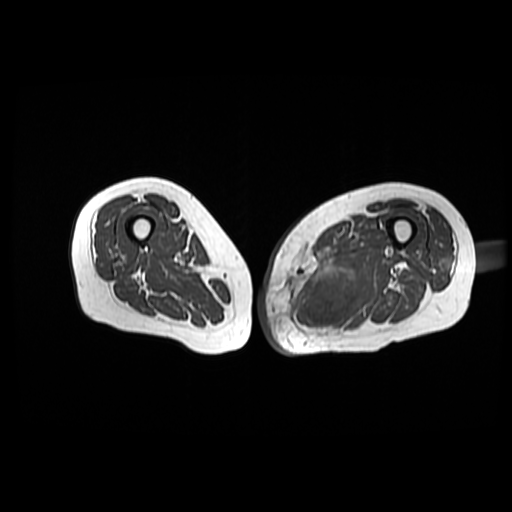
MRI of an extremity soft-tissue mass, one axial slice; position 36 of 42 along the scan axis; 6 mm slice thickness; 512 × 512 image matrix. Female patient. From the clinical record (not read from this slice): histological type: pleomorphic leiomyosarcoma; grade: high; site of the primary tumour: left thigh.
Annotated regions visible in this slice (manually delineated by an expert):
- gross tumour volume including surrounding oedema: bounding box (x1, y1, x2, y2) in pixels: (290, 241, 368, 331)
- gross tumour volume (mass): (300, 263, 364, 331)